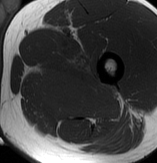
MRI of an extremity soft-tissue mass, one axial slice. Position 54 of 70 along the scan axis. MR volume resampled by the dataset authors to the PET/CT grid (not the native acquisition matrix). 157 × 163 image matrix, field of view 153 × 159 mm. Male patient. From the clinical record (not read from this slice): histological type: extraskeletal osteosarcoma; grade: high; site of the primary tumour: left adductur.
Outlined on this slice (expert contour drawn on MRI and transferred to this co-registered scan by the dataset authors):
- gross tumour volume (mass): bounding box (x1, y1, x2, y2) in pixels: (33, 51, 121, 121)